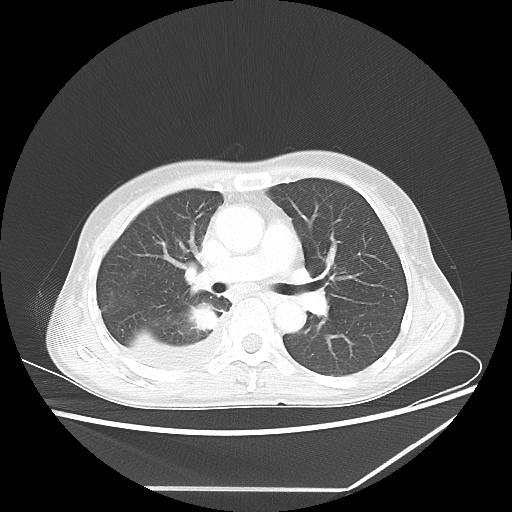
Chest CT, one axial slice; position 36 of 60 along the scan axis; reconstruction kernel LUNG; 80 kVp; lung window (W 1500 / L -600 HU); 5 mm slice thickness; 512 × 512 image matrix, field of view 364 × 364 mm. Patient: female, 59 years. From the clinical record (not read from this slice): clinical TNM (as recorded): T1c N1 M1.
Outlined on this slice (rectangle marked by the reading radiologist):
- lung tumour (recorded histology: adenocarcinoma): bounding box <187,301,216,332> (left, top, right, bottom; pixels)